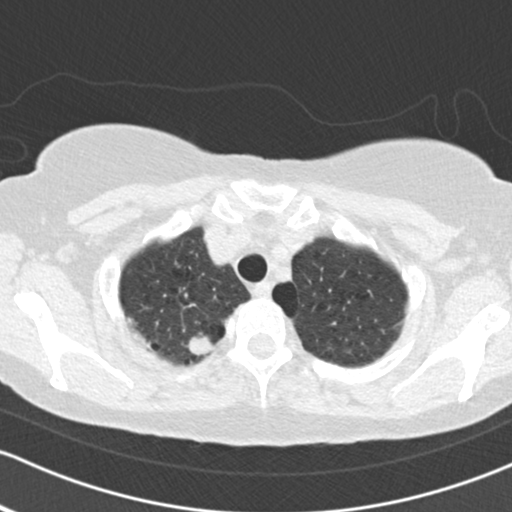
Low-dose screening chest CT, one axial slice. Position 144 of 161 along the scan axis. Reconstruction kernel B30f. 120 kVp. Lung window (W 1500 / L -600 HU). 512 × 512 image matrix, field of view 312 × 312 mm.
Structures marked on this image (expert manual segmentation):
- lesion 1 (tumor, upper lobe of right lung): box from (x=188, y=332) to (x=215, y=357) px